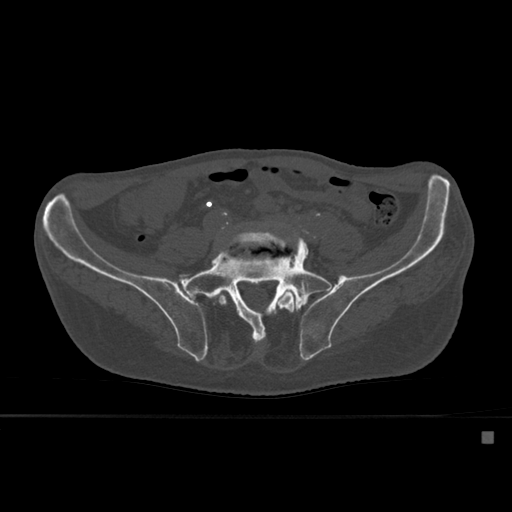
CT including the spine, one axial slice; slice 165 of 527 in the series (ordered by position); bone window (W 1800 / L 400 HU); 1.5 mm slice thickness; 512 × 512 image matrix. Patient: male, 78 years. Case-level facts recorded for this patient, not image findings: primary cancer: prostate.
Outlined on this slice (semi-automatic segmentation, software-assisted and operator-edited):
- L5 vertebra: bounding box [x1, y1, x2, y2] px = [213, 229, 296, 313]